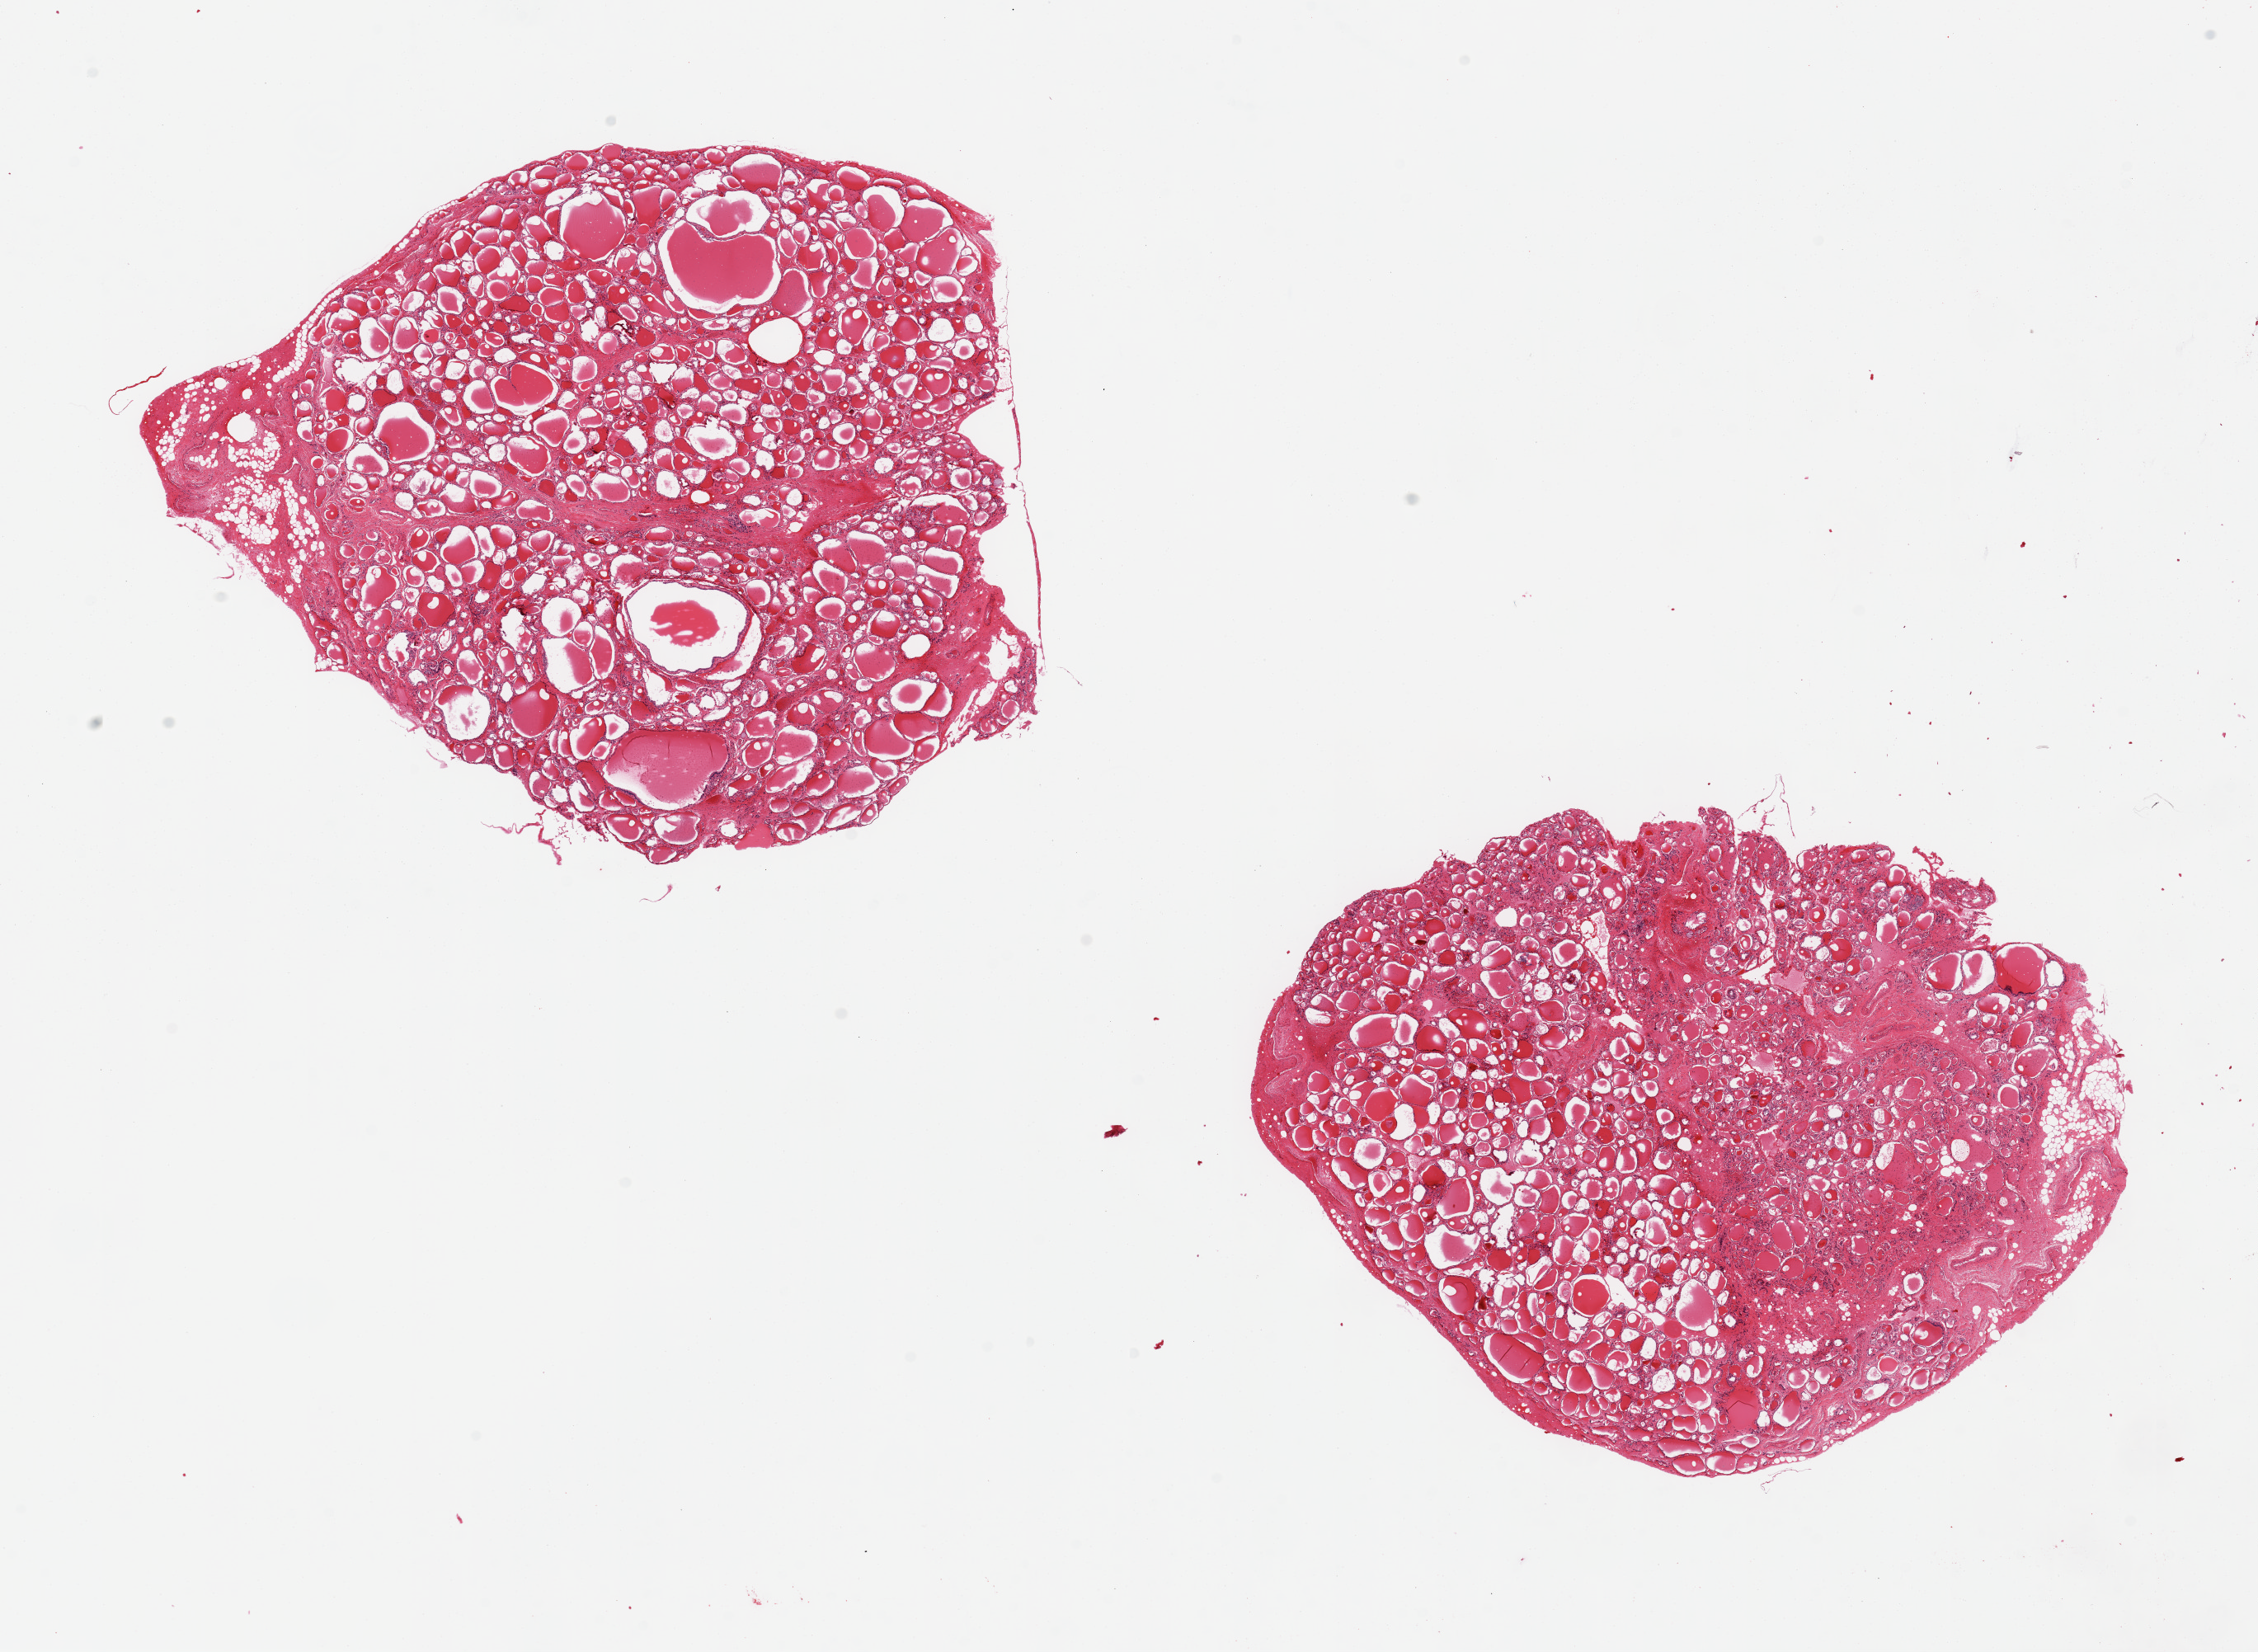
Whole-slide image, hematoxylin and eosin (H&E) stain — low-resolution overview of the scanned area, about 21.7 x 15.8 mm. PAXgene-fixed paraffin-embedded (PFPE) section. Target tissue: thyroid. Tissue donor sample. Female donor.
• pathologist's review note for this sample: 2 pieces, ~5-10% of each is fat and fibrous/vascular tissue, regressive change